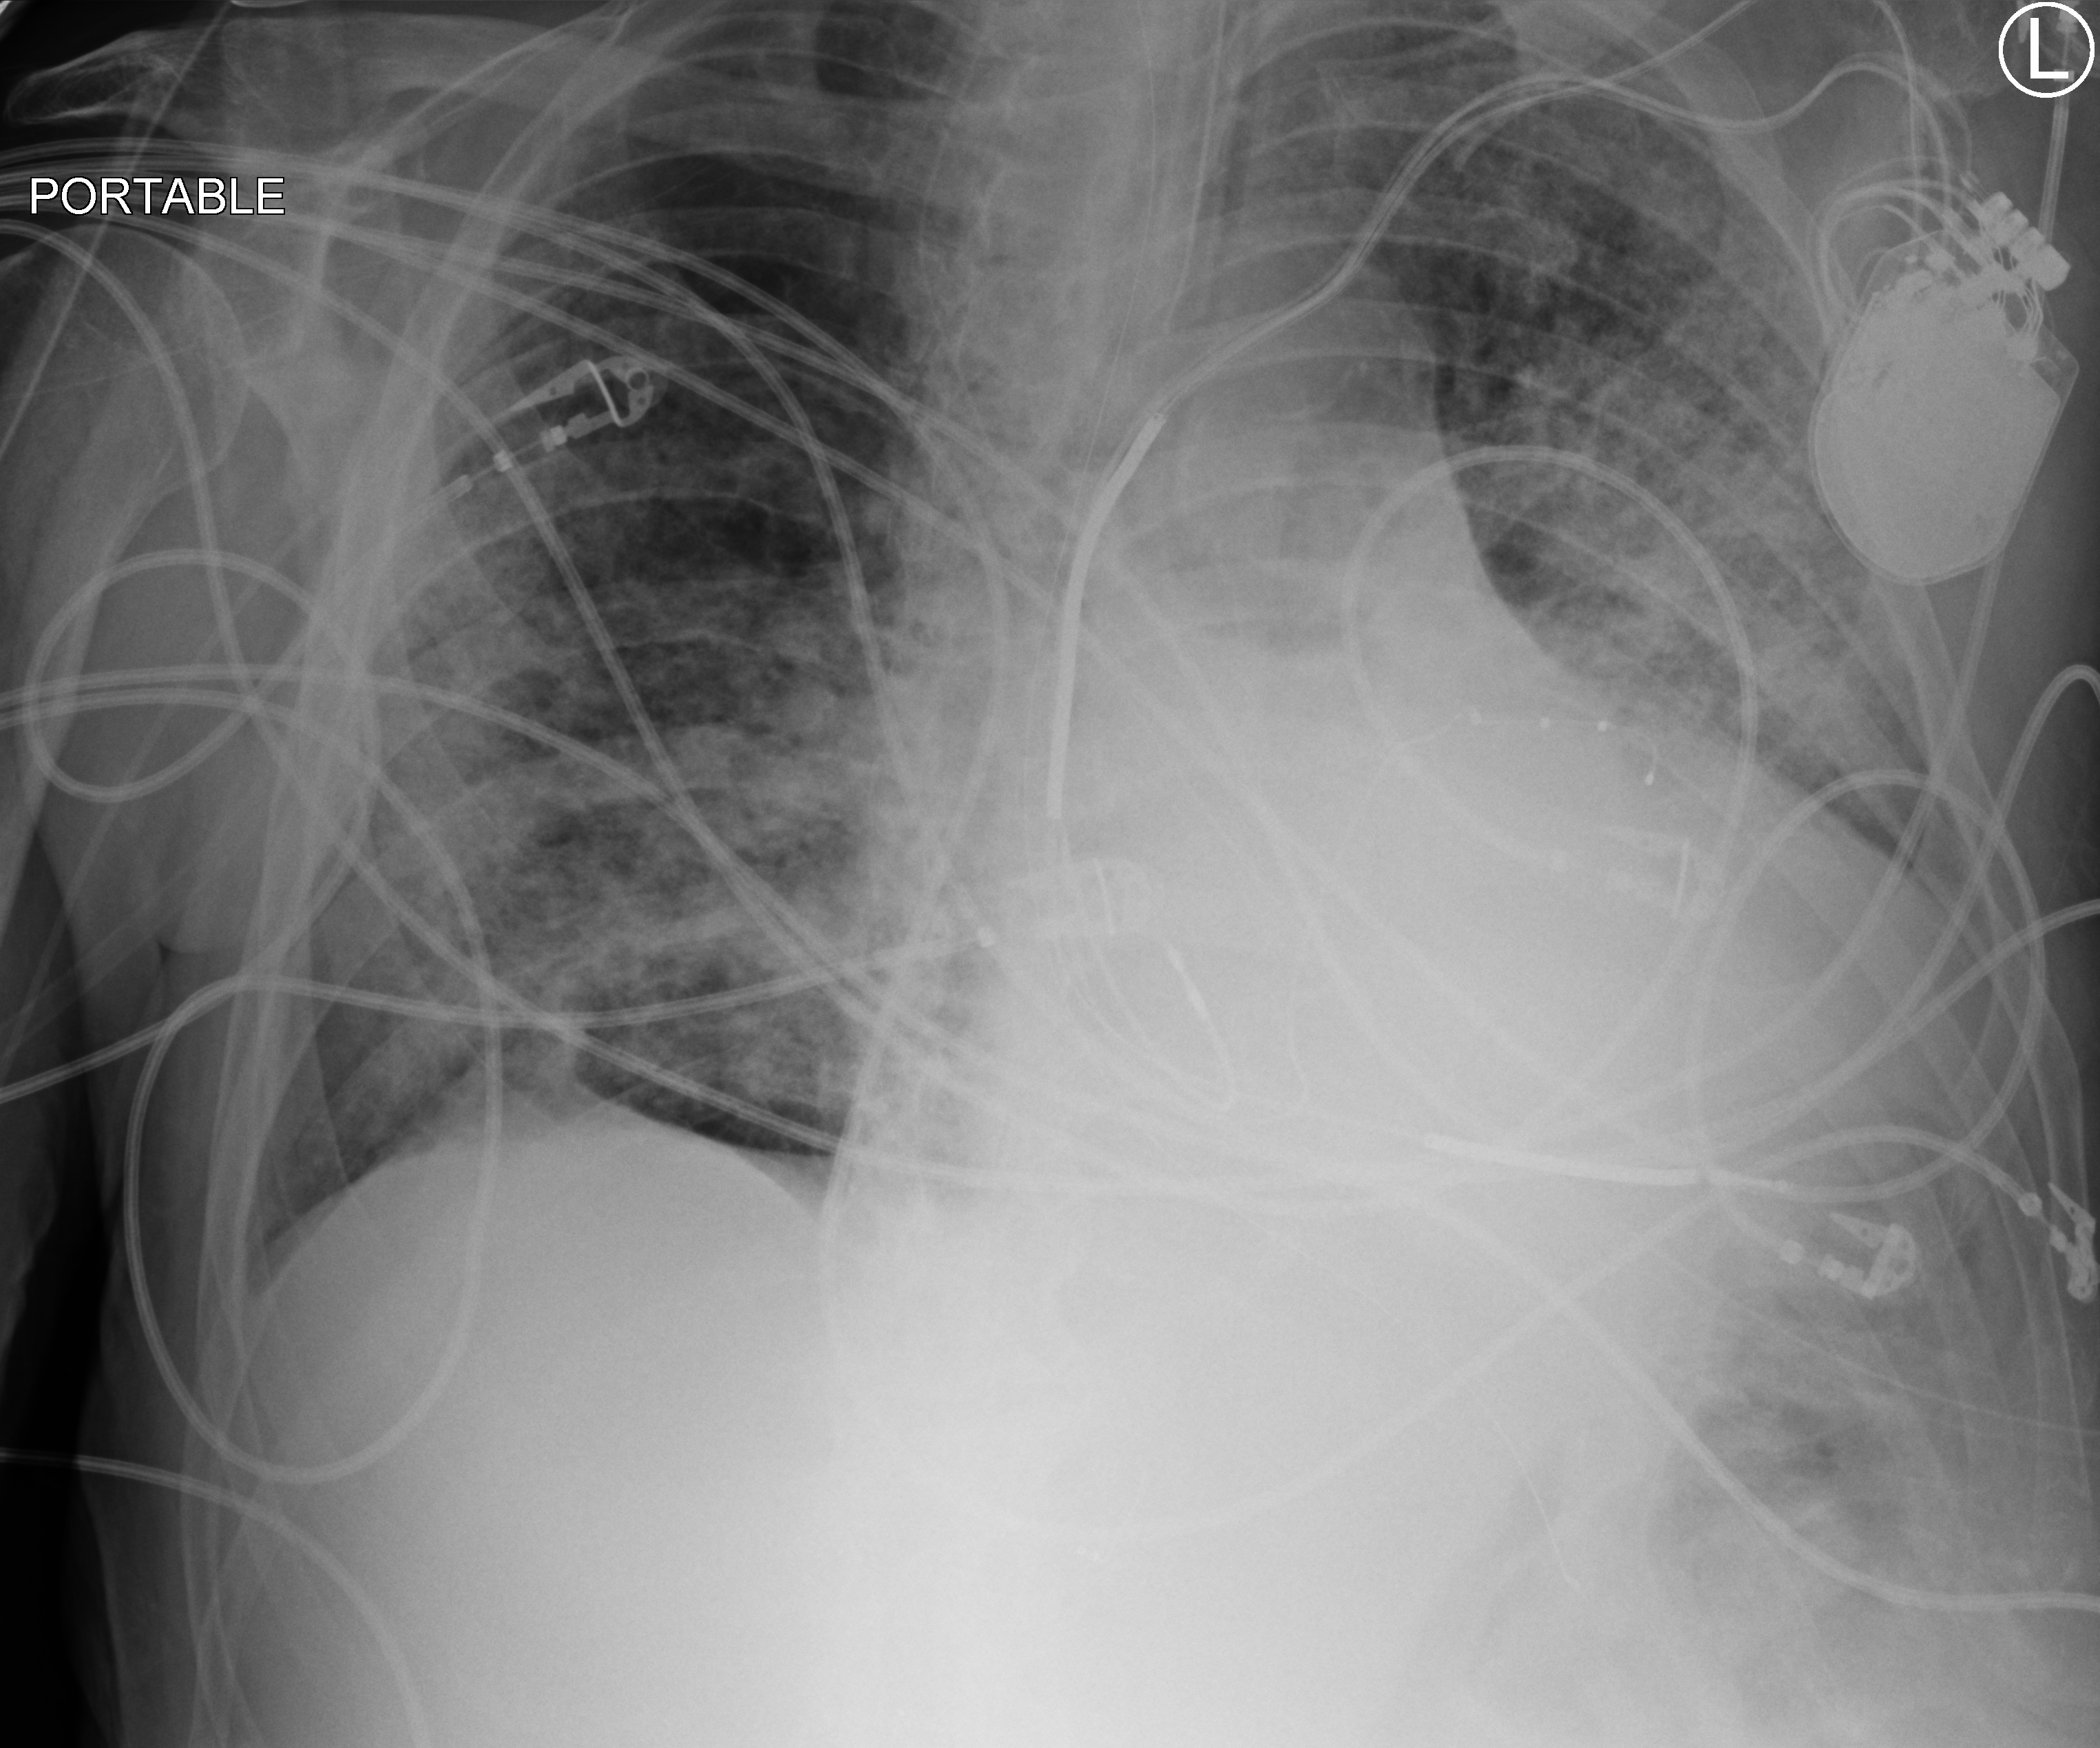
Portable chest radiograph, anteroposterior (AP) projection. Patient hospitalised with COVID-19; male, aged 60–74 years.
Admission-level facts for this patient (not findings on this image; timing relative to this image not recorded): COPD (admission record): no; mechanically ventilated during this hospital stay: yes; length of hospital stay: 36 days.